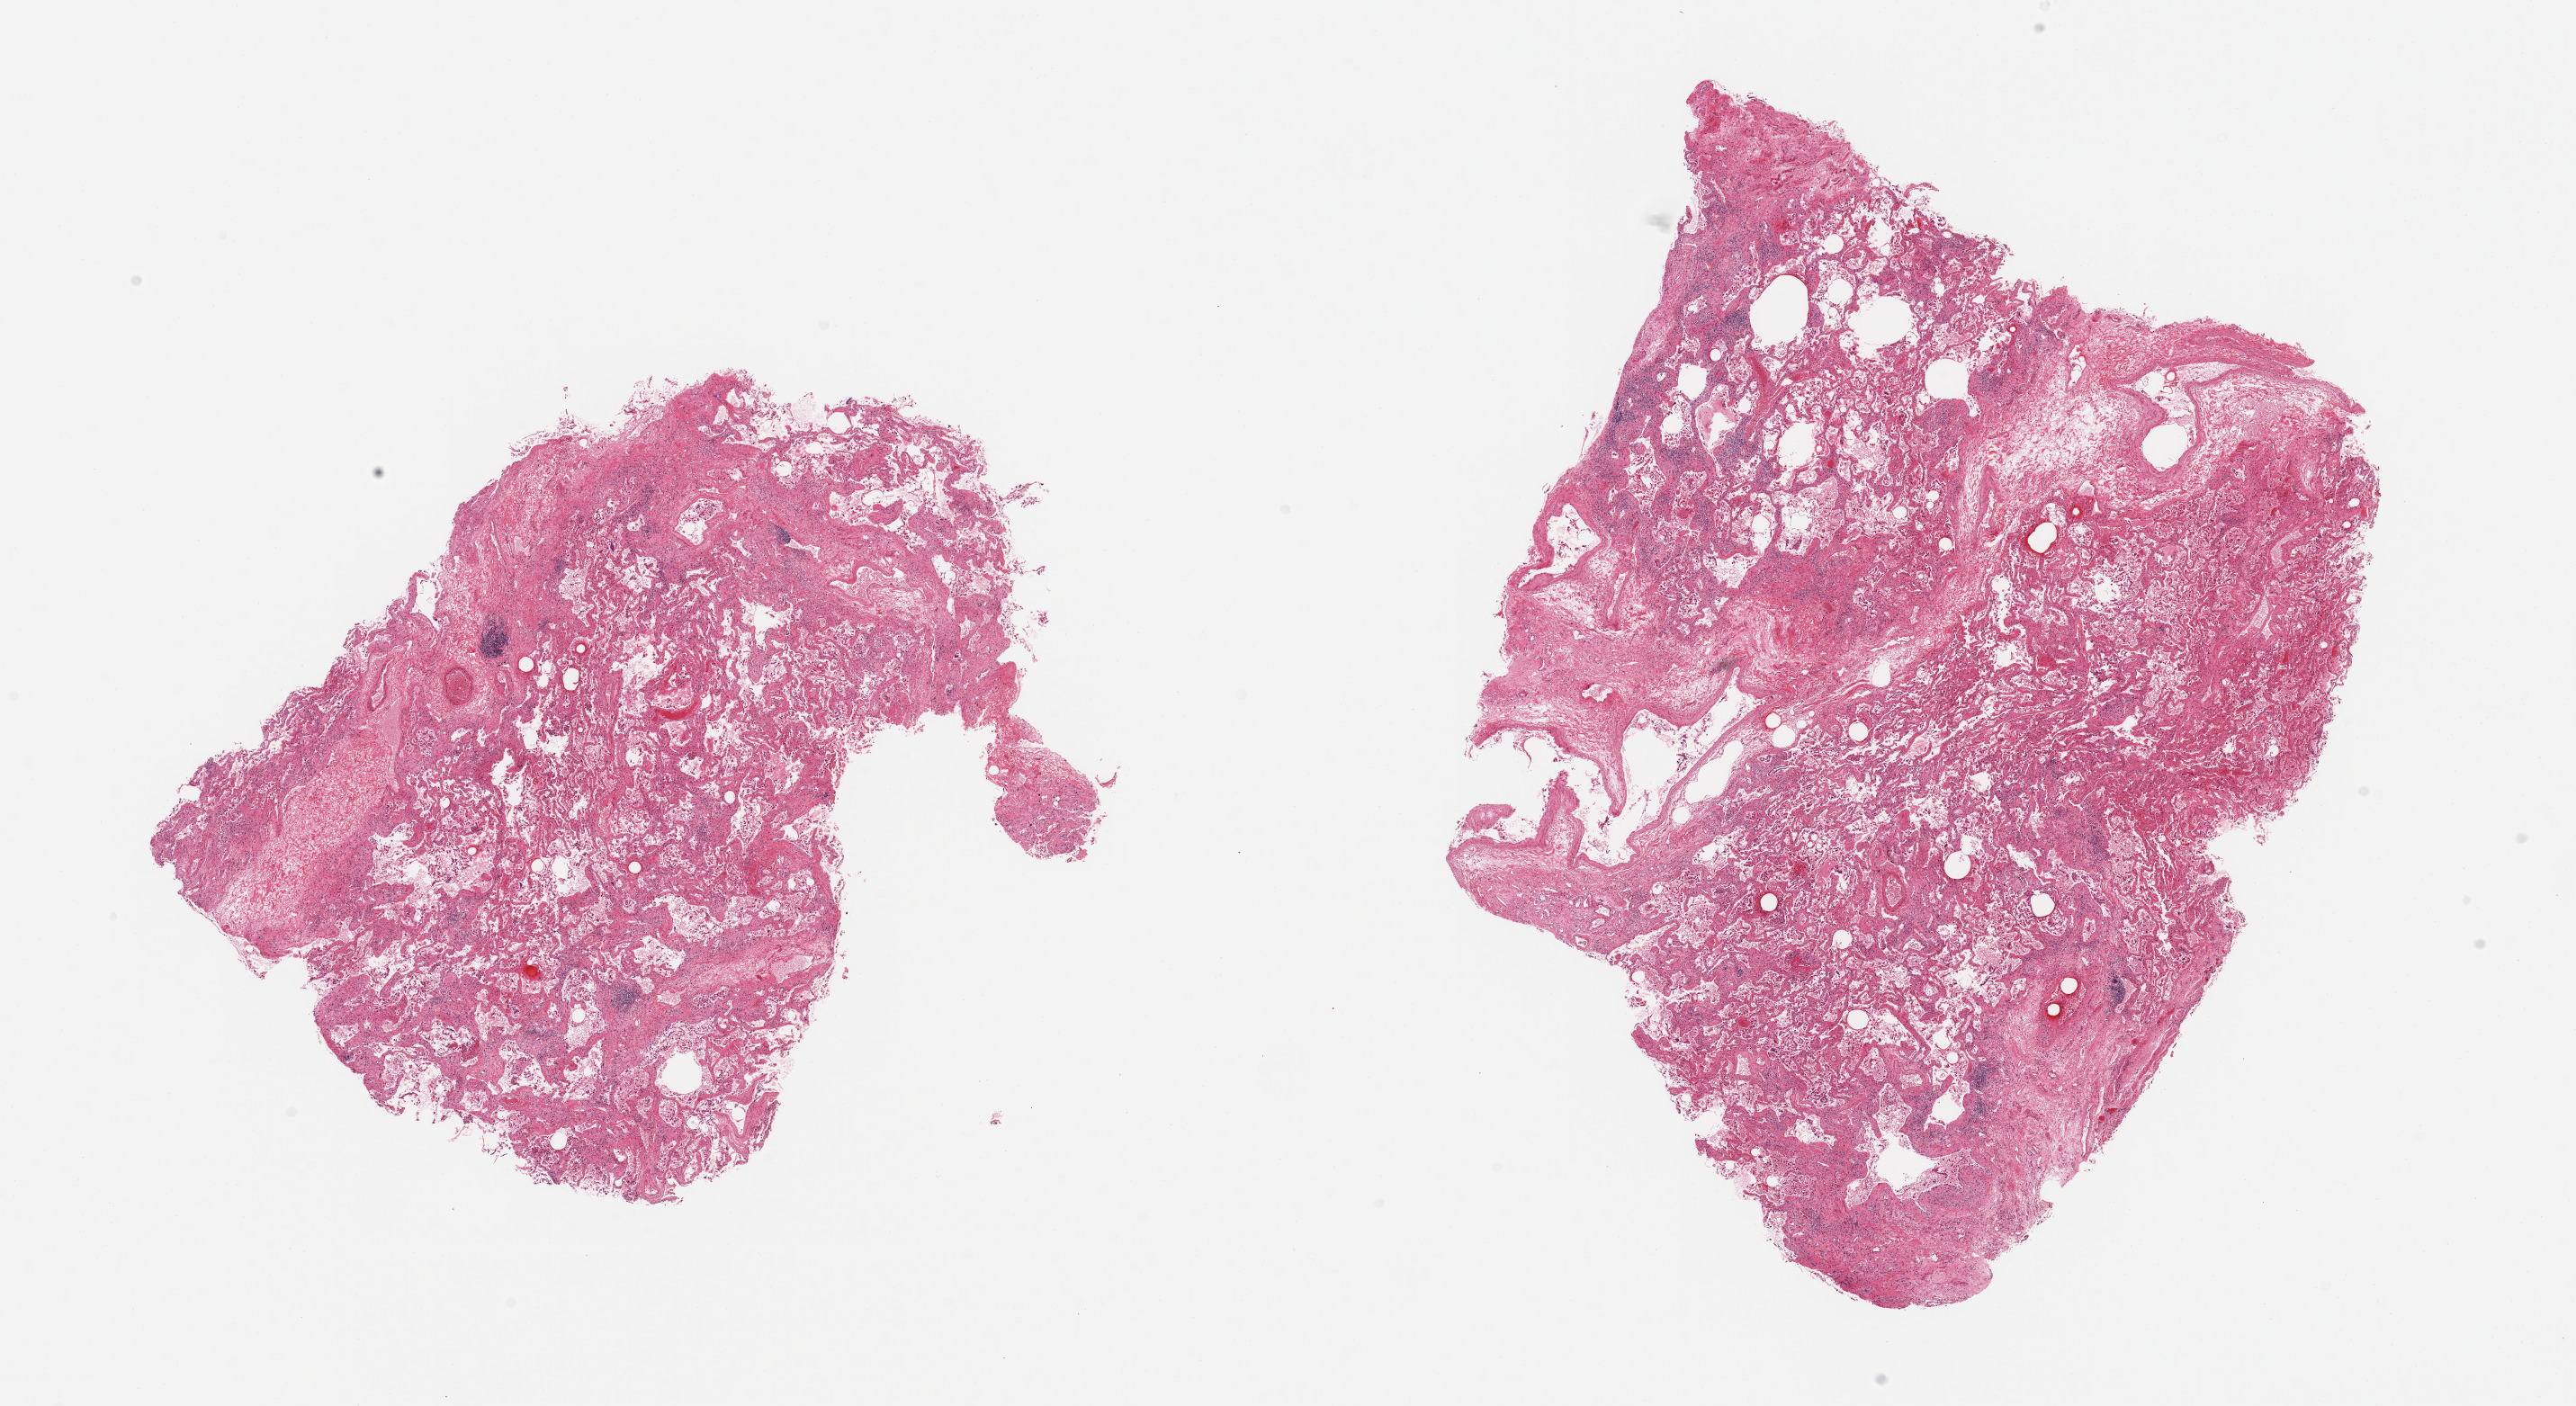
Whole-slide image, H&E stain, whole scanned area (about 22.6 x 12.4 mm) shown as a low-resolution overview. PAXgene-fixed, paraffin-embedded tissue. Section of lung (target tissue). Tissue donor sample. Donor sex: male.
• reviewer comment on this tissue sample: 2 pieces chronic fibrosing pneumonitis; edema